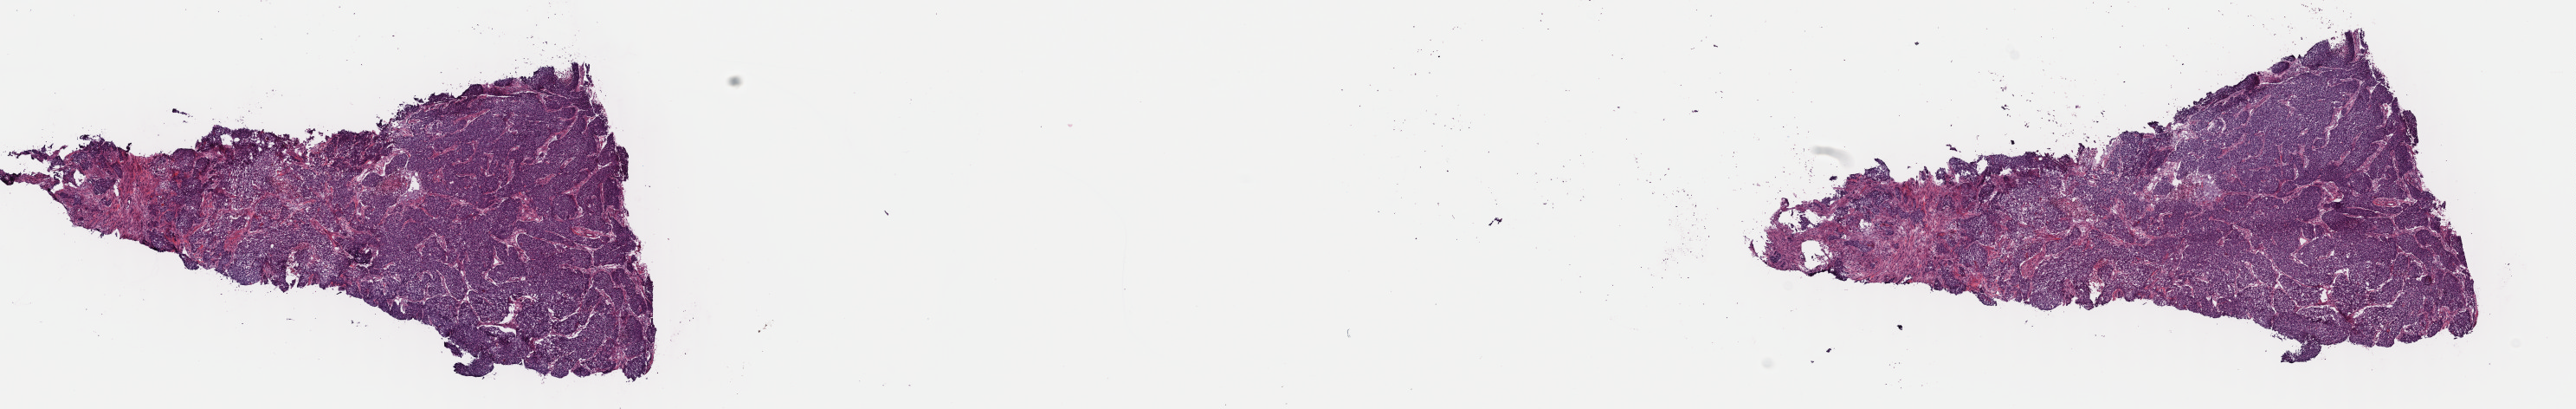
Digitized Hematoxylin and eosin (H&E) stained tissue section (whole slide) — shown as a low-resolution overview of the whole scanned area (about 23.5 x 3.7 mm, slide scanned at 40x); frozen section from the top of the tissue portion; sample: primary tumour, cervix. Female, age 33 years at initial diagnosis. Histologic grade: G2 (moderately differentiated). Pathologist review of this section (percent, as recorded): tumour cells 80%, tumour nuclei 80%, normal cells 0%, stromal cells 15%, necrosis 5%. Infiltration values recorded for this section: lymphocyte infiltration 1%, monocyte infiltration 1%, neutrophil infiltration 1%.
FIGO stage: IB1. Diagnosis: Adenosquamous carcinoma (cervix uteri).